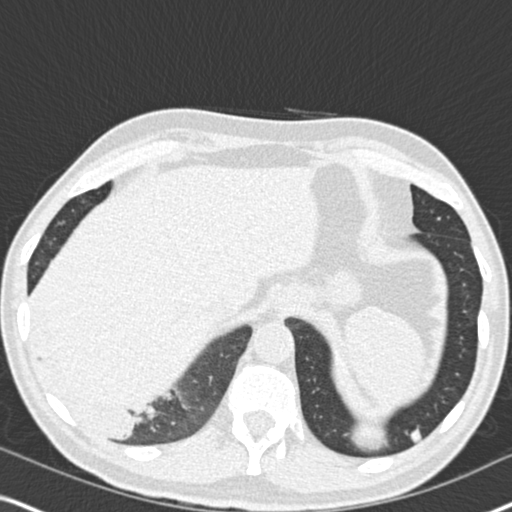
Low-dose screening chest CT, one axial slice. Position 47 of 182 along the scan axis. Reconstruction kernel B30f. 120 kVp. Lung window (W 1500 / L -600 HU). 2 mm slice thickness. 512 × 512 image matrix, field of view 330 × 330 mm.
Structures marked on this image (outlined manually by an expert reader):
- lesion 1 (tumor, lower lobe of right lung): box from (x=83, y=400) to (x=140, y=437) px